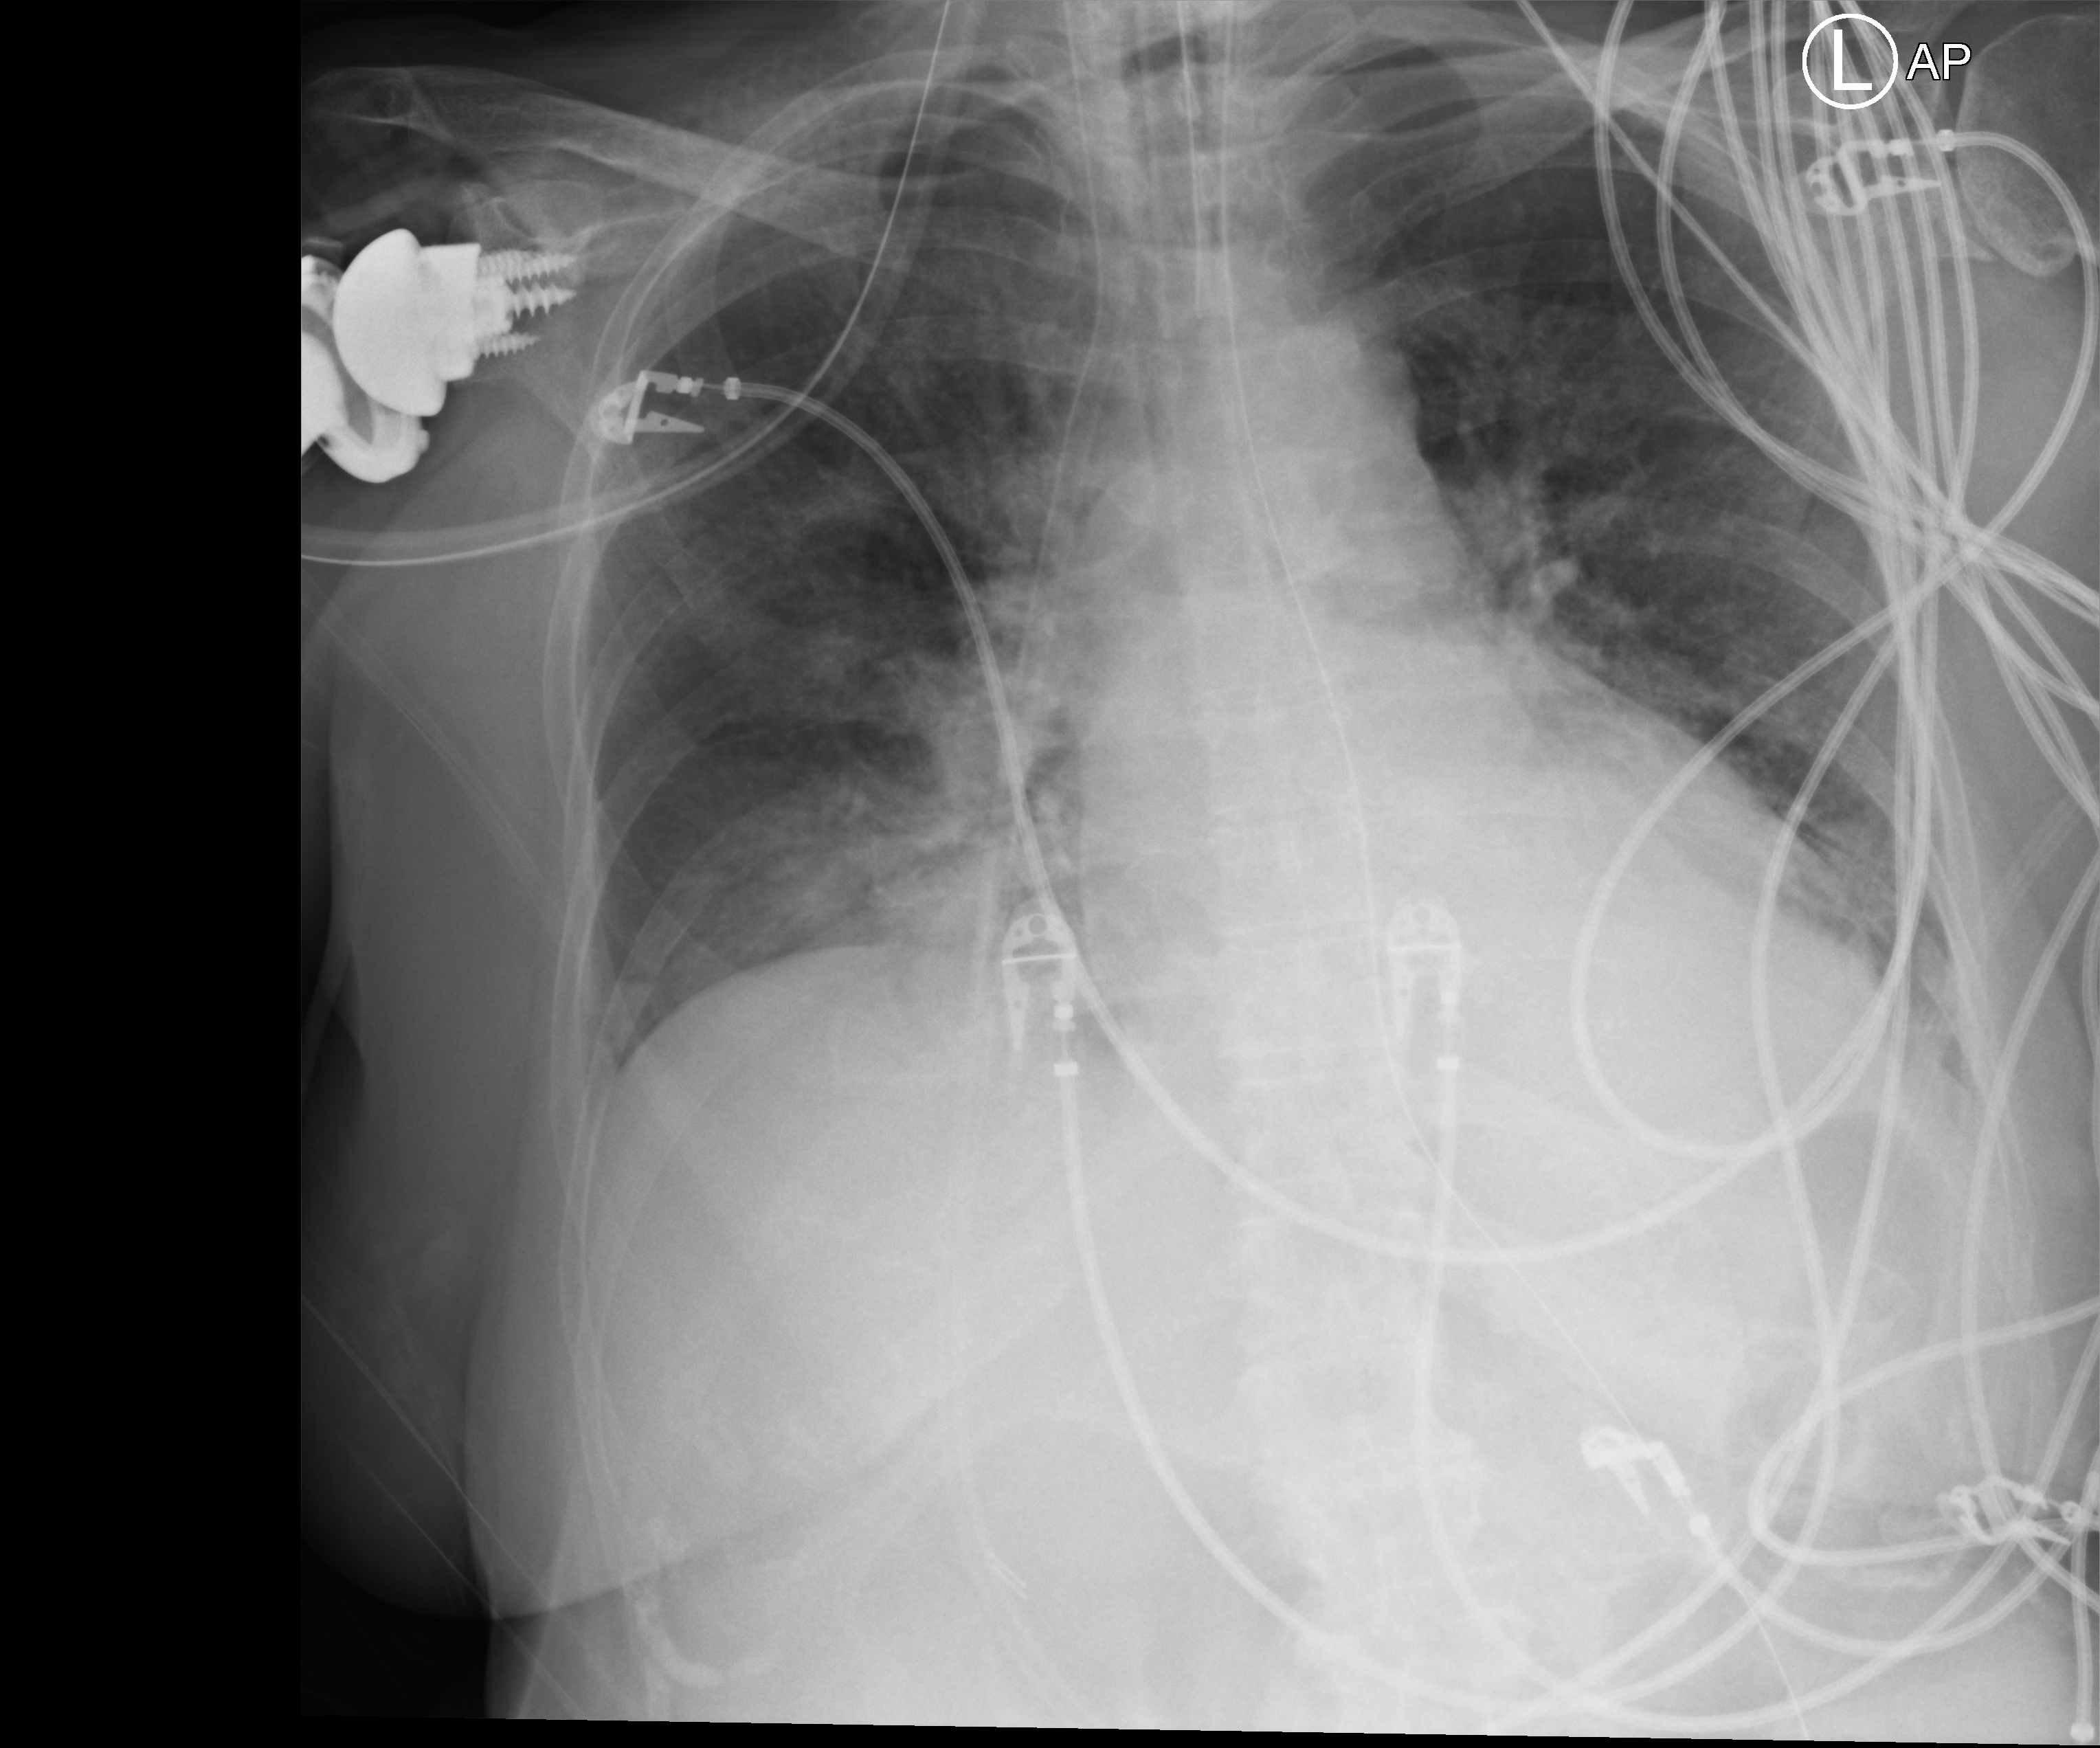
Bedside chest radiograph (computed radiography); anteroposterior (AP) projection. Patient hospitalised with COVID-19; female, aged 60–74 years.
Admission-level facts for this patient (not findings on this image; timing relative to this image not recorded): admitted to intensive care during this hospital stay: yes; length of hospital stay: 27 days; mechanically ventilated during this hospital stay: yes.